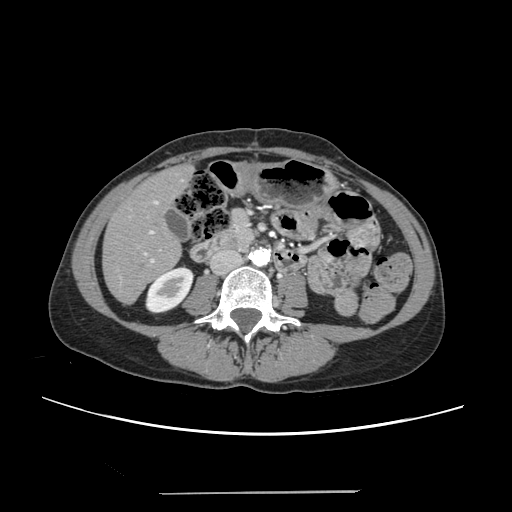
Contrast-enhanced abdominal CT, one axial slice. Slice 74 of 240 in the series (ordered by position). Intravenous contrast given. Soft-tissue window (W 400 / L 40 HU). 1.25 mm slice thickness. 512 × 512 image matrix. Female patient, age 60 years. Case-level facts recorded for this patient, not image findings: diagnosis: colorectal cancer liver metastases, imaged before liver resection; multiple liver metastases: no; largest metastasis: 1.5 cm; disease in both lobes: no.
Structures marked on this image (outlined manually by an expert reader):
- liver: bounding box [x1, y1, x2, y2] px = [104, 166, 192, 302]
- planned liver remnant (the part of the liver to remain after resection): [104, 172, 180, 302]
- portal vein (with intrahepatic branches): [143, 200, 161, 262]